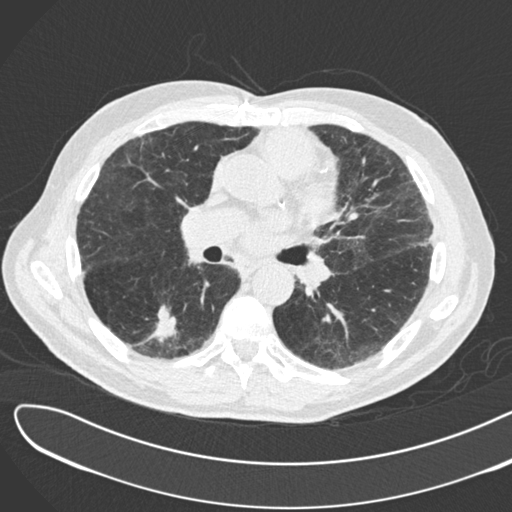
Chest CT (low-dose screening protocol), one axial image, second annual screen, lung window (W 1500 / L -600 HU), 2 mm slice thickness, standard (soft-tissue) reconstruction kernel (B30f), slice 92 of 183 in the series, 512 × 512 image matrix. Male participant, aged 72 years at enrolment. Former smoker at enrolment.
• Expert reader's lesion annotation, bounding box <135,292,193,348> (left, top, right, bottom; pixels).
• The screening reader recorded 2 non-calcified nodules or masses ≥4 mm on this exam (right lower lobe, right lower lobe); which of them this box marks is not recorded.
• Official screen result: positive, change unspecified: nodule(s) >= 4 mm or enlarging nodule(s), mass(es), or other non-specific abnormalities suspicious for lung cancer.